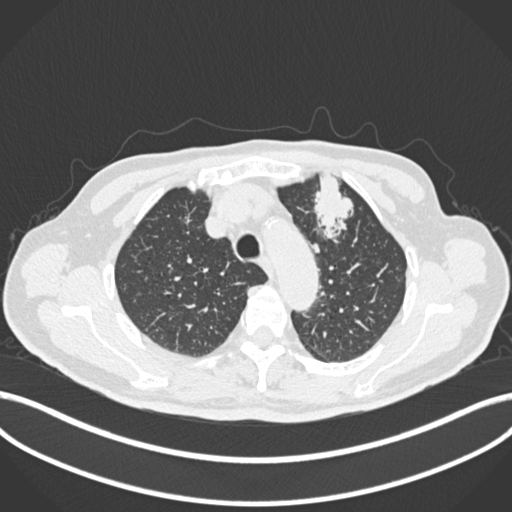
Chest CT, one axial slice; position 202 of 261 along the scan axis; 120 kVp; lung window (W 1500 / L -600 HU); 1 mm slice thickness; 512 × 512 image matrix, field of view 400 × 400 mm. Male patient, age 74 years. Case-level facts recorded for this patient, not image findings: clinical TNM (as recorded): T2b N0 M1c.
Structures marked on this image (rectangle marked by the reading radiologist):
- lung tumour (recorded histology: adenocarcinoma): bounding box (x1, y1, x2, y2) in pixels: (310, 170, 358, 241)